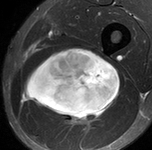
MRI of an extremity soft-tissue mass, one axial slice; slice 62 of 90 in the series (ordered by position); STIR; MR volume resampled by the dataset authors to the PET/CT grid (not the native acquisition matrix); 152 × 150 image matrix, field of view 148 × 146 mm. Male patient. From the clinical record (not read from this slice): histological type: undifferentiated pleomorphic liposarcoma; grade: high; site of the primary tumour: left thigh.
Structures marked on this image (expert contour drawn on MRI and transferred to this co-registered scan by the dataset authors):
- gross tumour volume including surrounding oedema: bounding box <22,48,122,127> (left, top, right, bottom; pixels)
- gross tumour volume (mass): <22,48,122,124>